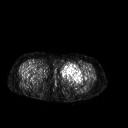
FDG PET of an extremity soft-tissue mass (from a PET/CT study), one axial slice; position 245 of 267 along the scan axis; 3.27 mm slice thickness; 128 × 128 image matrix. Female patient, age 42 years. From the clinical record (not read from this slice): histological type: pleiomorphic leiomyosarcoma; grade: intermediate; site of the primary tumour: left thigh.
Outlined on this slice (expert contour drawn on MRI and transferred to this co-registered scan by the dataset authors):
- gross tumour volume including surrounding oedema: bounding box (x1, y1, x2, y2) in pixels: (59, 64, 82, 82)
- gross tumour volume (mass): (59, 64, 82, 82)